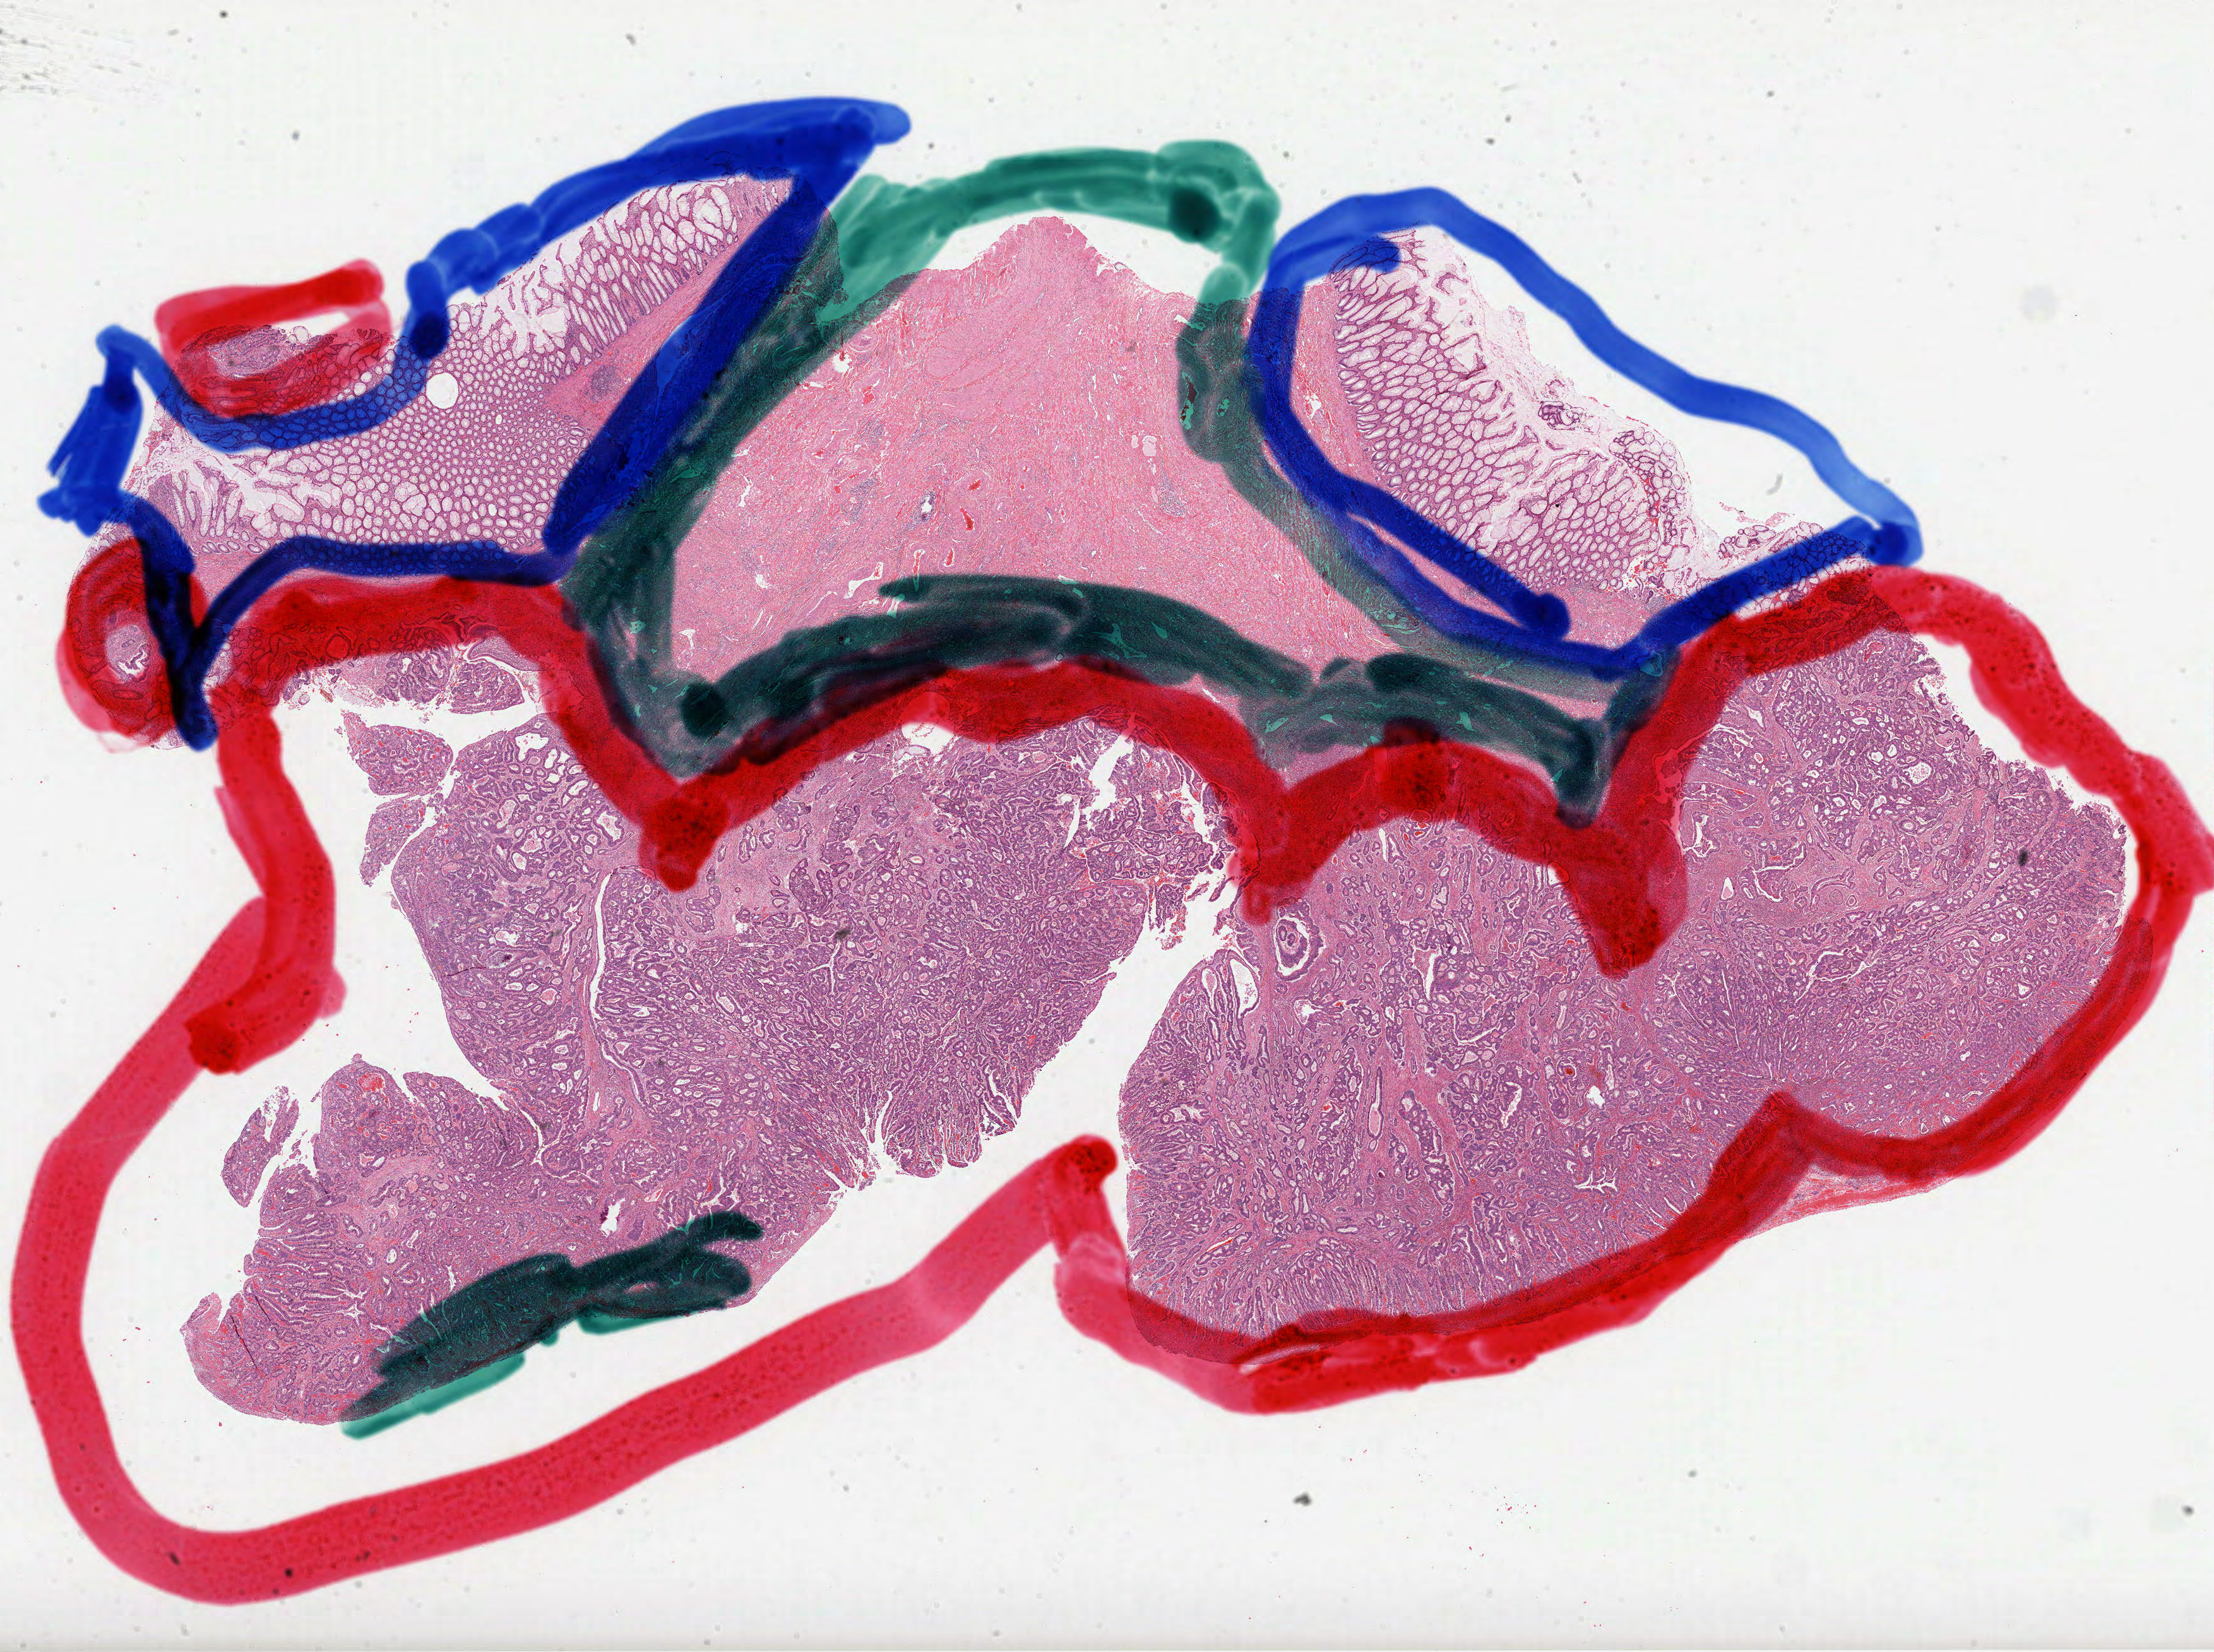
Whole-slide histology image, H&E — whole scanned area (about 28.3 x 21.1 mm) shown as a low-resolution overview. Formalin-fixed paraffin-embedded (FFPE) diagnostic section. Primary tumour sample from the colon. Patient: female, age at initial diagnosis 54 years.
• histologic diagnosis: Adenocarcinoma, NOS (sigmoid colon)
• lymph nodes positive (case pathology): 0 of 3 examined
• AJCC pathologic stage: I